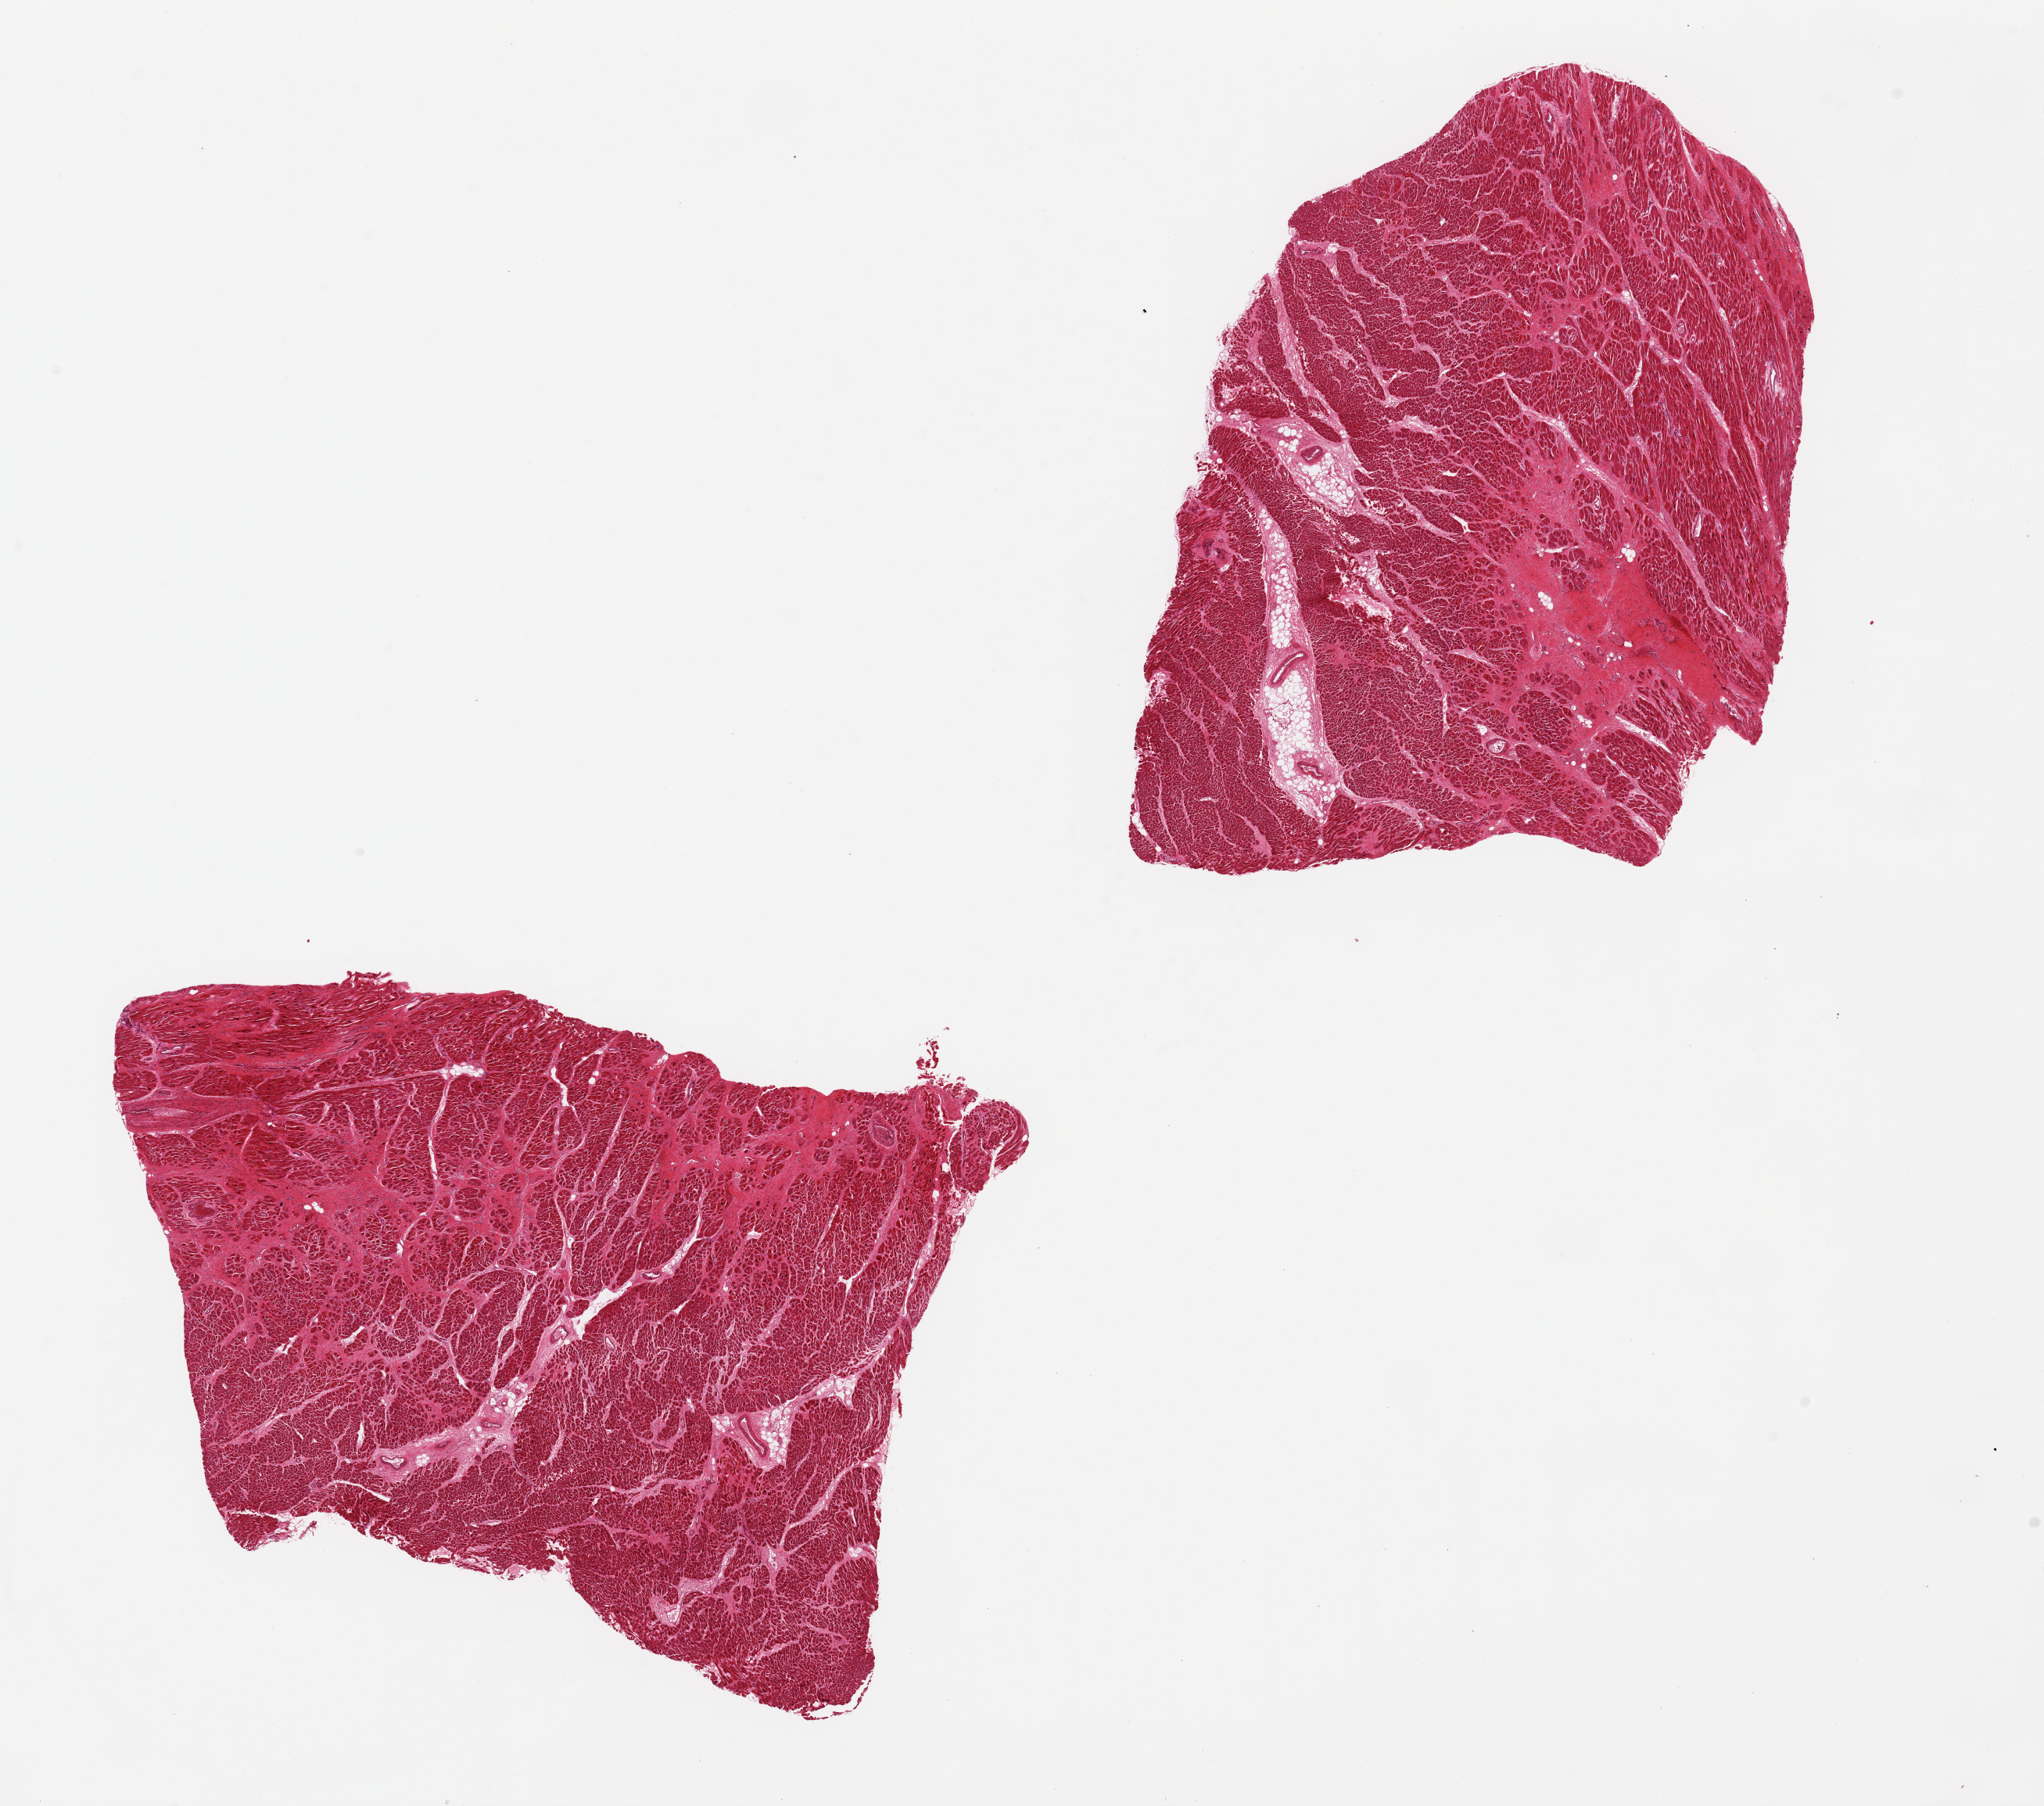
Digitized hematoxylin and eosin (H&E)-stained section, brightfield — low-resolution overview of the scanned area, about 20.7 x 18.3 mm (slide scanned at 20x); PAXgene-fixed, paraffin-embedded tissue; section of heart (target tissue); donor tissue sample. Male donor.
Review note (as recorded): 2 pieces. 9x7 & 8.5x6mm; multiple ~3-4mm fibrotic infarcts noted.